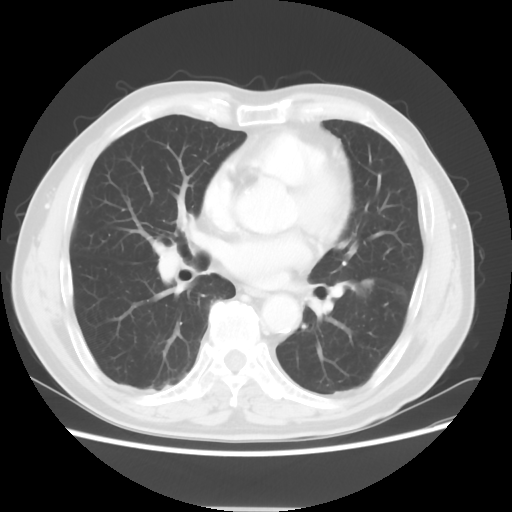
Chest CT, one axial slice; slice 27 of 64 in the series (ordered by position); reconstruction kernel STANDARD; 120 kVp; lung window (W 1500 / L -600 HU); 5 mm slice thickness; 512 × 512 image matrix. Male patient, age 71 years. Case-level facts recorded for this patient, not image findings: clinical TNM (as recorded): T1c N1 M0; histopathological grade: G2-3.
Structures marked on this image (rectangle marked by the reading radiologist):
- lung tumour (recorded histology: adenocarcinoma): bounding box (x1, y1, x2, y2) in pixels: (352, 268, 381, 303)